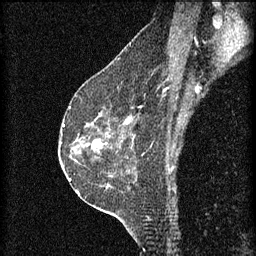
Breast MRI (dynamic contrast-enhanced), one sagittal slice; 3 images stored at this slice position (order not interpretable as contrast timing); 1.5 T; TE 4.2 ms, TR 8.2 ms; 256 × 256 image matrix, field of view 180 × 180 mm. Female patient, age 60 years.
Outlined on this slice (semi-automatically segmented with operator editing):
- analysis volume of interest (the breast-tissue region the enhancement analysis was run in; not a lesion): bounding box (x1, y1, x2, y2) in pixels: (74, 124, 113, 159)
- tumour enhancement mask (voxels above the 70 % enhancement threshold inside the analysis volume of interest): (94, 142, 103, 147)